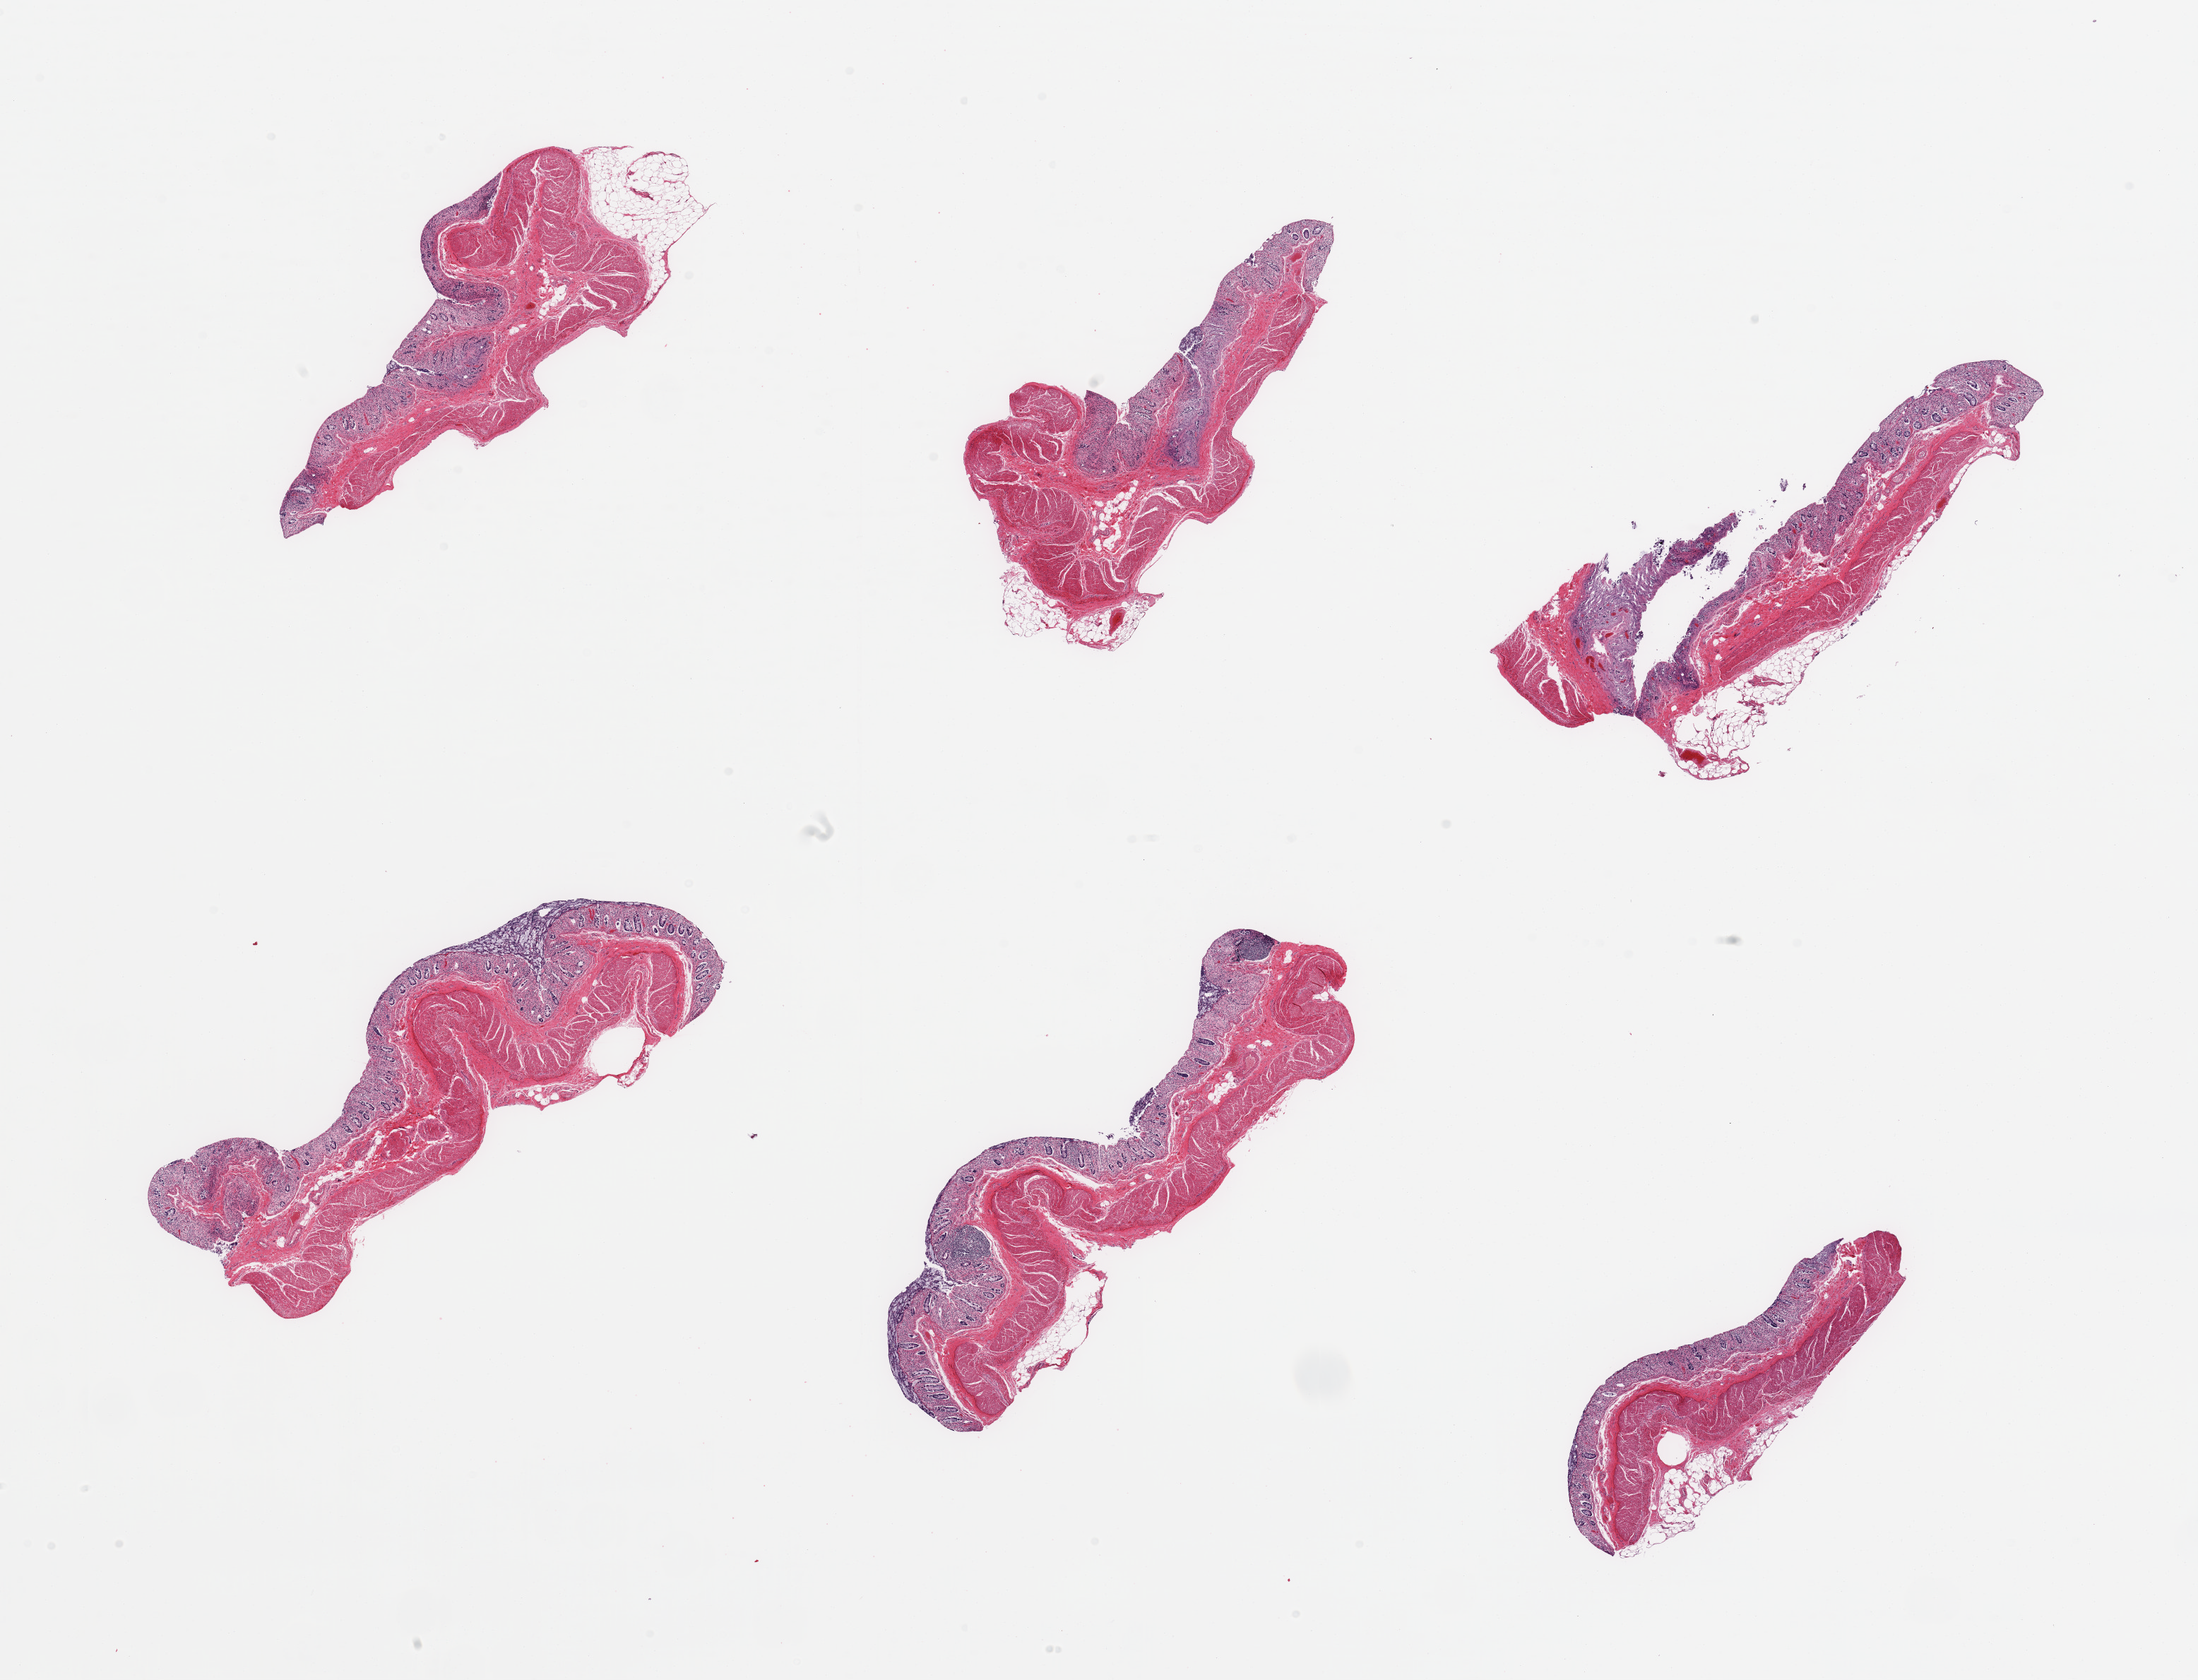
H&E whole-slide image, low-resolution overview of the scanned area, about 24.6 x 18.8 mm (acquisition: 20x scan). PAXgene-fixed, paraffin-embedded tissue. Sampled site (target tissue): sigmoid colon. Donor tissue sample. Female donor.
Pathologist's review note for this sample: 6 pieces; full thickness sections of colon, mucosa largely autolyzed.